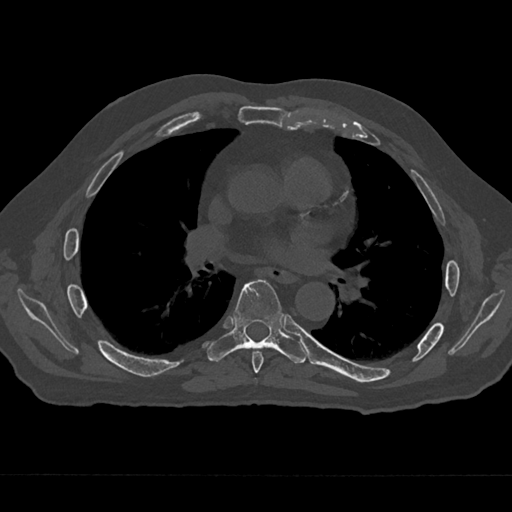
CT including the spine, one axial slice. Slice 387 of 797 in the series (ordered by position). Reconstruction kernel Br40s/3. 120 kVp. Bone window (W 1800 / L 400 HU). 0.5 mm slice thickness. 512 × 512 image matrix, field of view 377 × 377 mm. Male patient, age 75 years. Case-level facts recorded for this patient, not image findings: primary cancer: renal; vertebrae with lytic lesions (as recorded): T4.
Structures marked on this image (semi-automatic segmentation, software-assisted and operator-edited):
- T6 vertebra: box from (x=252, y=351) to (x=264, y=373) px
- T7 vertebra: (x=207, y=279)–(x=306, y=364)